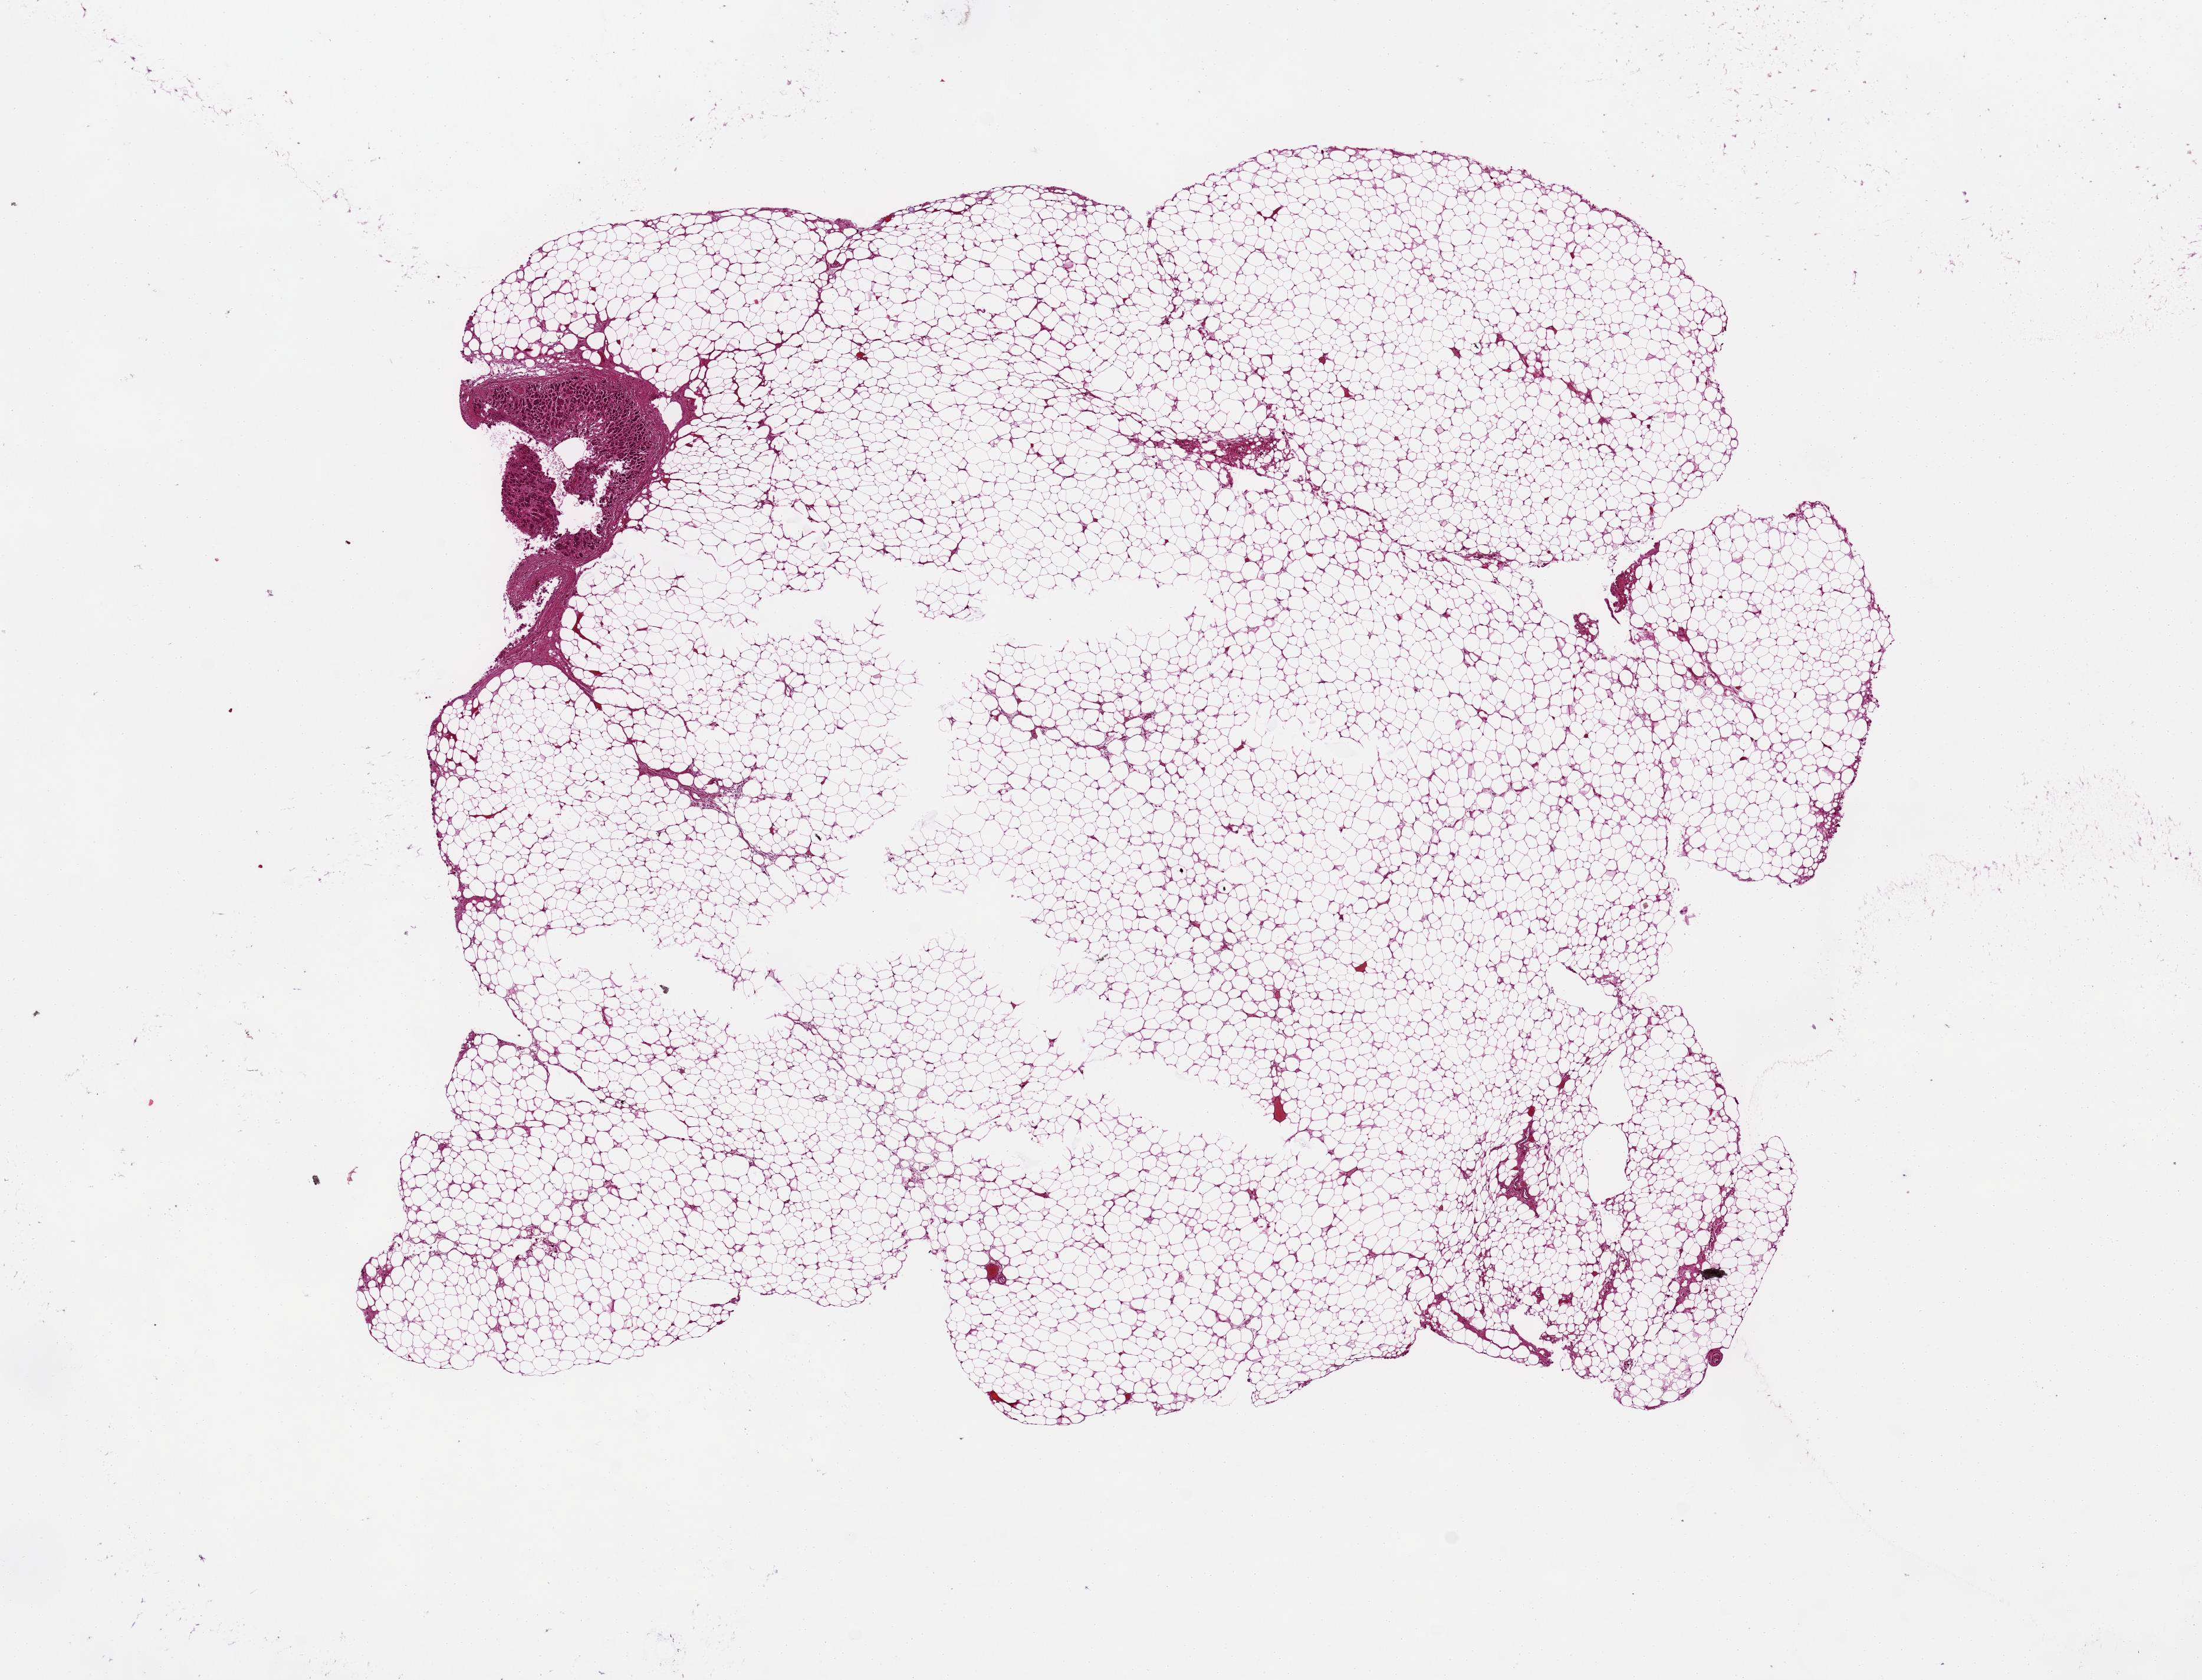
Digitized haematoxylin and eosin-stained section, shown as a low-resolution overview of the whole scanned area (about 14.8 x 11.3 mm, from a 20x scan), PAXgene-fixed paraffin-embedded (PFPE) section, target tissue: adrenal gland, tissue donor sample. Donor sex: male.
Reviewer comment on this tissue sample: 95% aliquot is fat (centrally unfixed).